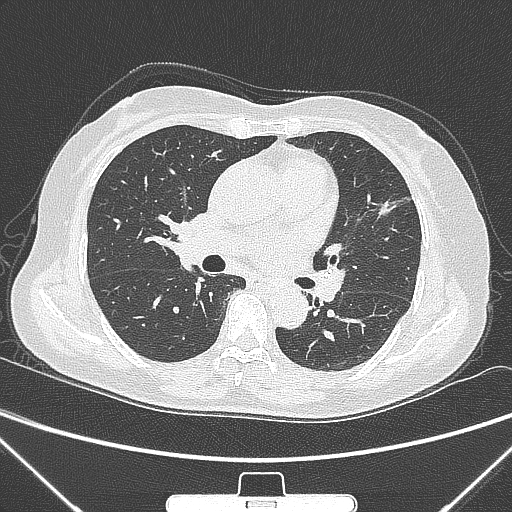
Chest CT, one axial slice. Slice 152 of 300 in the series (ordered by position). Lung window (W 1500 / L -600 HU). 1 mm slice thickness. 512 × 512 image matrix. Female patient, age 70 years. From the clinical record (not read from this slice): clinical TNM (as recorded): T1b N0 M0; histopathological grade: G2.
Structures marked on this image (rectangle marked by the reading radiologist):
- lung tumour (recorded histology: adenocarcinoma): box from (x=371, y=196) to (x=404, y=224) px